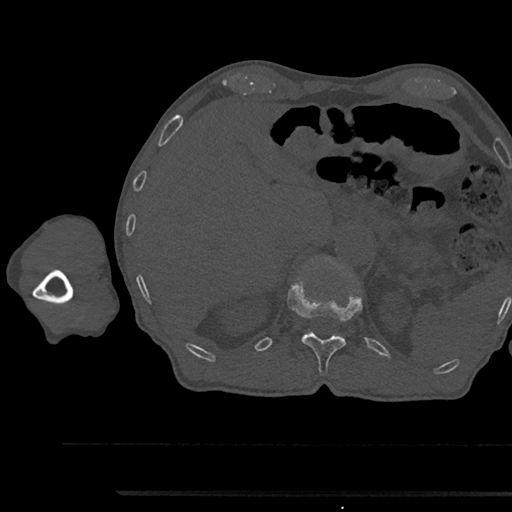
CT including the spine, one axial slice; position 699 of 797 along the scan axis; reconstruction kernel Br40s/3; bone window (W 1800 / L 400 HU); 0.5 mm slice thickness; 512 × 512 image matrix, field of view 367 × 367 mm. Male patient, age 79 years. Case-level facts recorded for this patient, not image findings: primary cancer: prostate.
Structures marked on this image (semi-automatically segmented with operator editing):
- T12 vertebra: box from (x=287, y=284) to (x=362, y=373) px